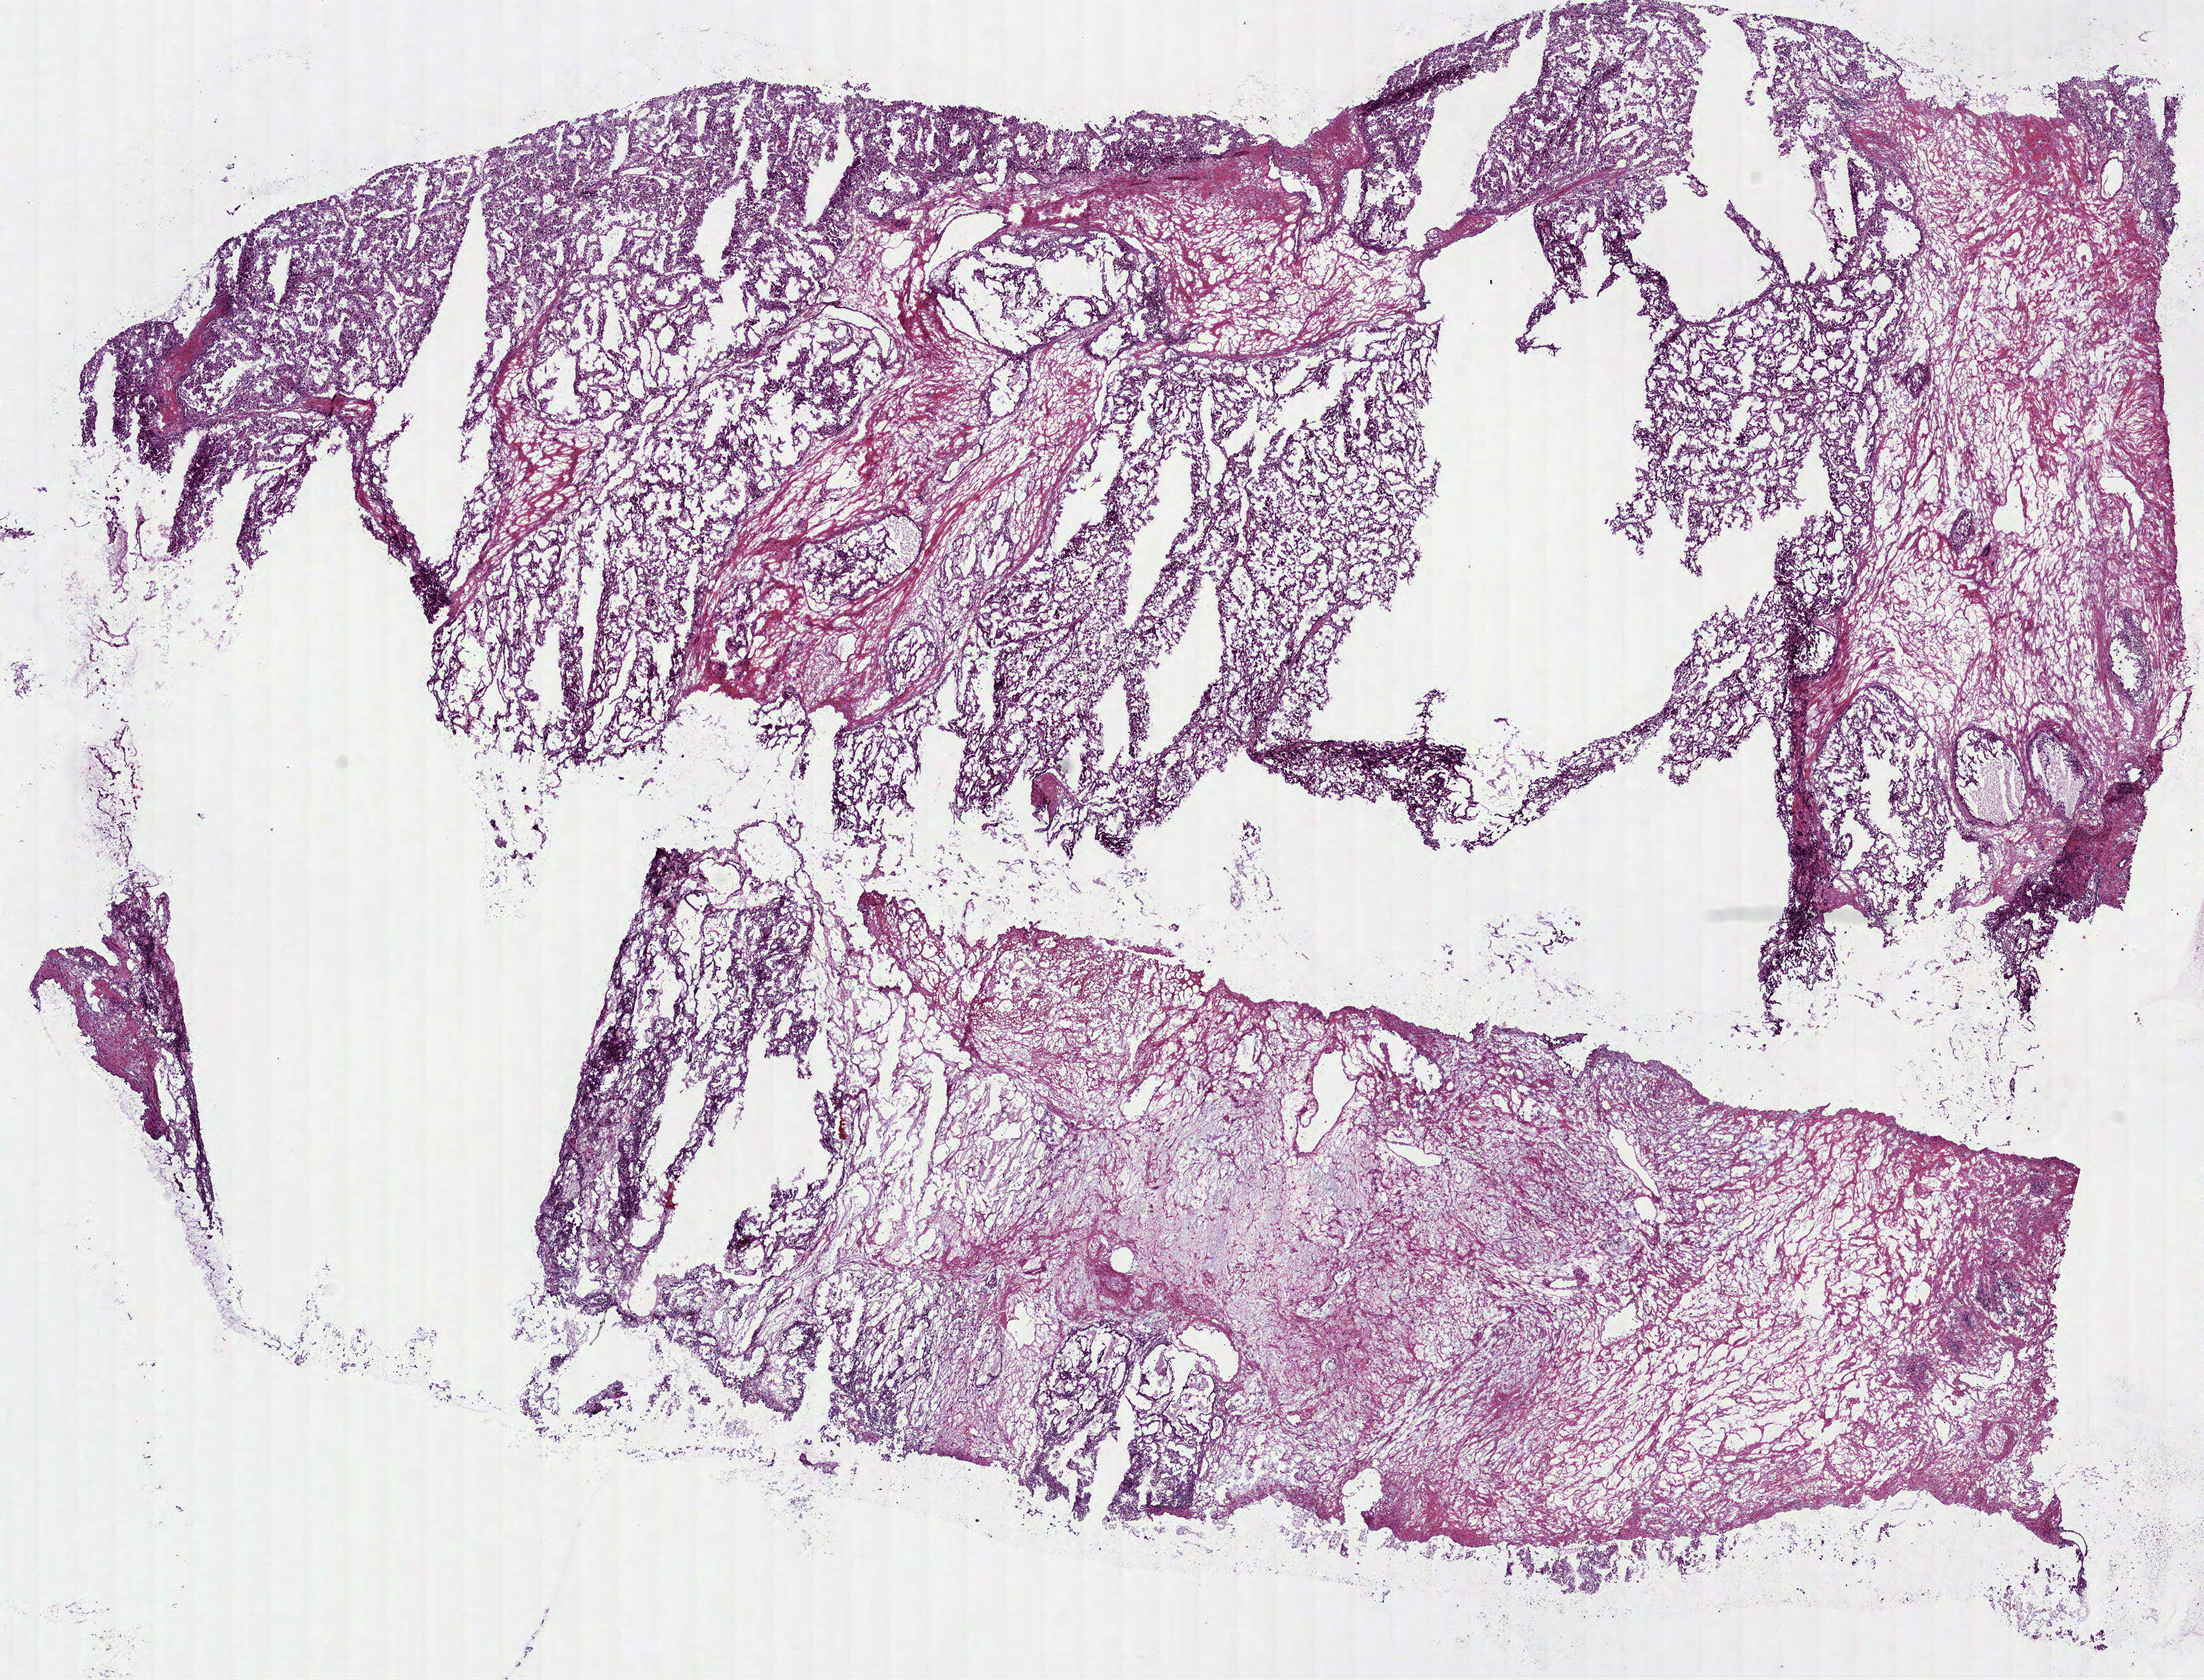
Whole-slide histology image, H&E, shown as a low-resolution overview of the whole scanned area (about 13.8 x 10.5 mm); frozen section from the bottom of the tissue portion; primary tumour sample from the kidney. Male, age 51 years at initial diagnosis. Pathologist review of this section (percent, as recorded): tumour cells 50%, tumour nuclei 80%, normal cells 0%, stromal cells 50%, necrosis 0%.
Lymph nodes positive (case pathology): 0 of 21 examined. Laterality: left. Diagnosis: Papillary adenocarcinoma, NOS. AJCC pathologic stage: I.